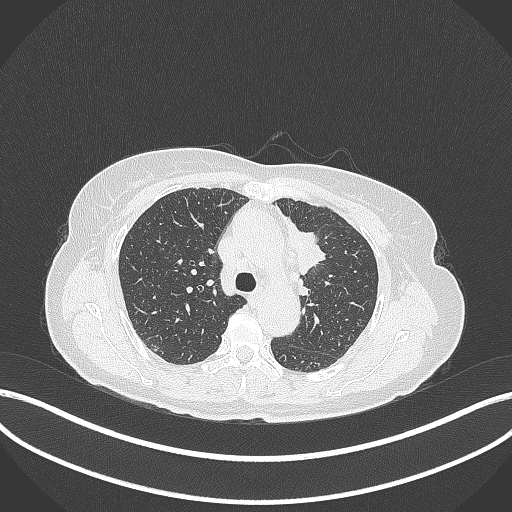
Chest CT, one axial slice. Slice 234 of 369 in the series (ordered by position). 120 kVp. Lung window (W 1500 / L -600 HU). 512 × 512 image matrix. Patient: female, 65 years. From the clinical record (not read from this slice): clinical TNM (as recorded): T2a N0 M0; histopathological grade: G2-3.
Structures marked on this image (bounding box drawn by a radiologist):
- lung tumour (recorded histology: adenocarcinoma): bounding box [x1, y1, x2, y2] px = [281, 212, 326, 275]